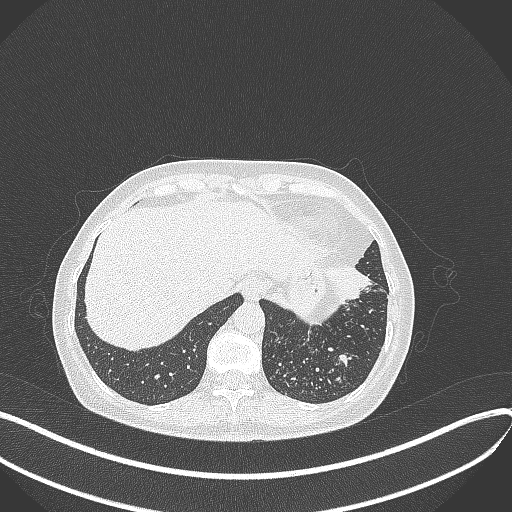
Chest CT, one axial slice; position 81 of 429 along the scan axis; 100 kVp; lung window (W 1500 / L -600 HU); 1 mm slice thickness; 512 × 512 image matrix, field of view 400 × 400 mm. Female patient, age 63 years. From the clinical record (not read from this slice): clinical TNM (as recorded): T1b N0 M0.
Structures marked on this image (bounding box drawn by a radiologist):
- lung tumour (recorded histology: adenocarcinoma): box from (x=323, y=264) to (x=371, y=304) px